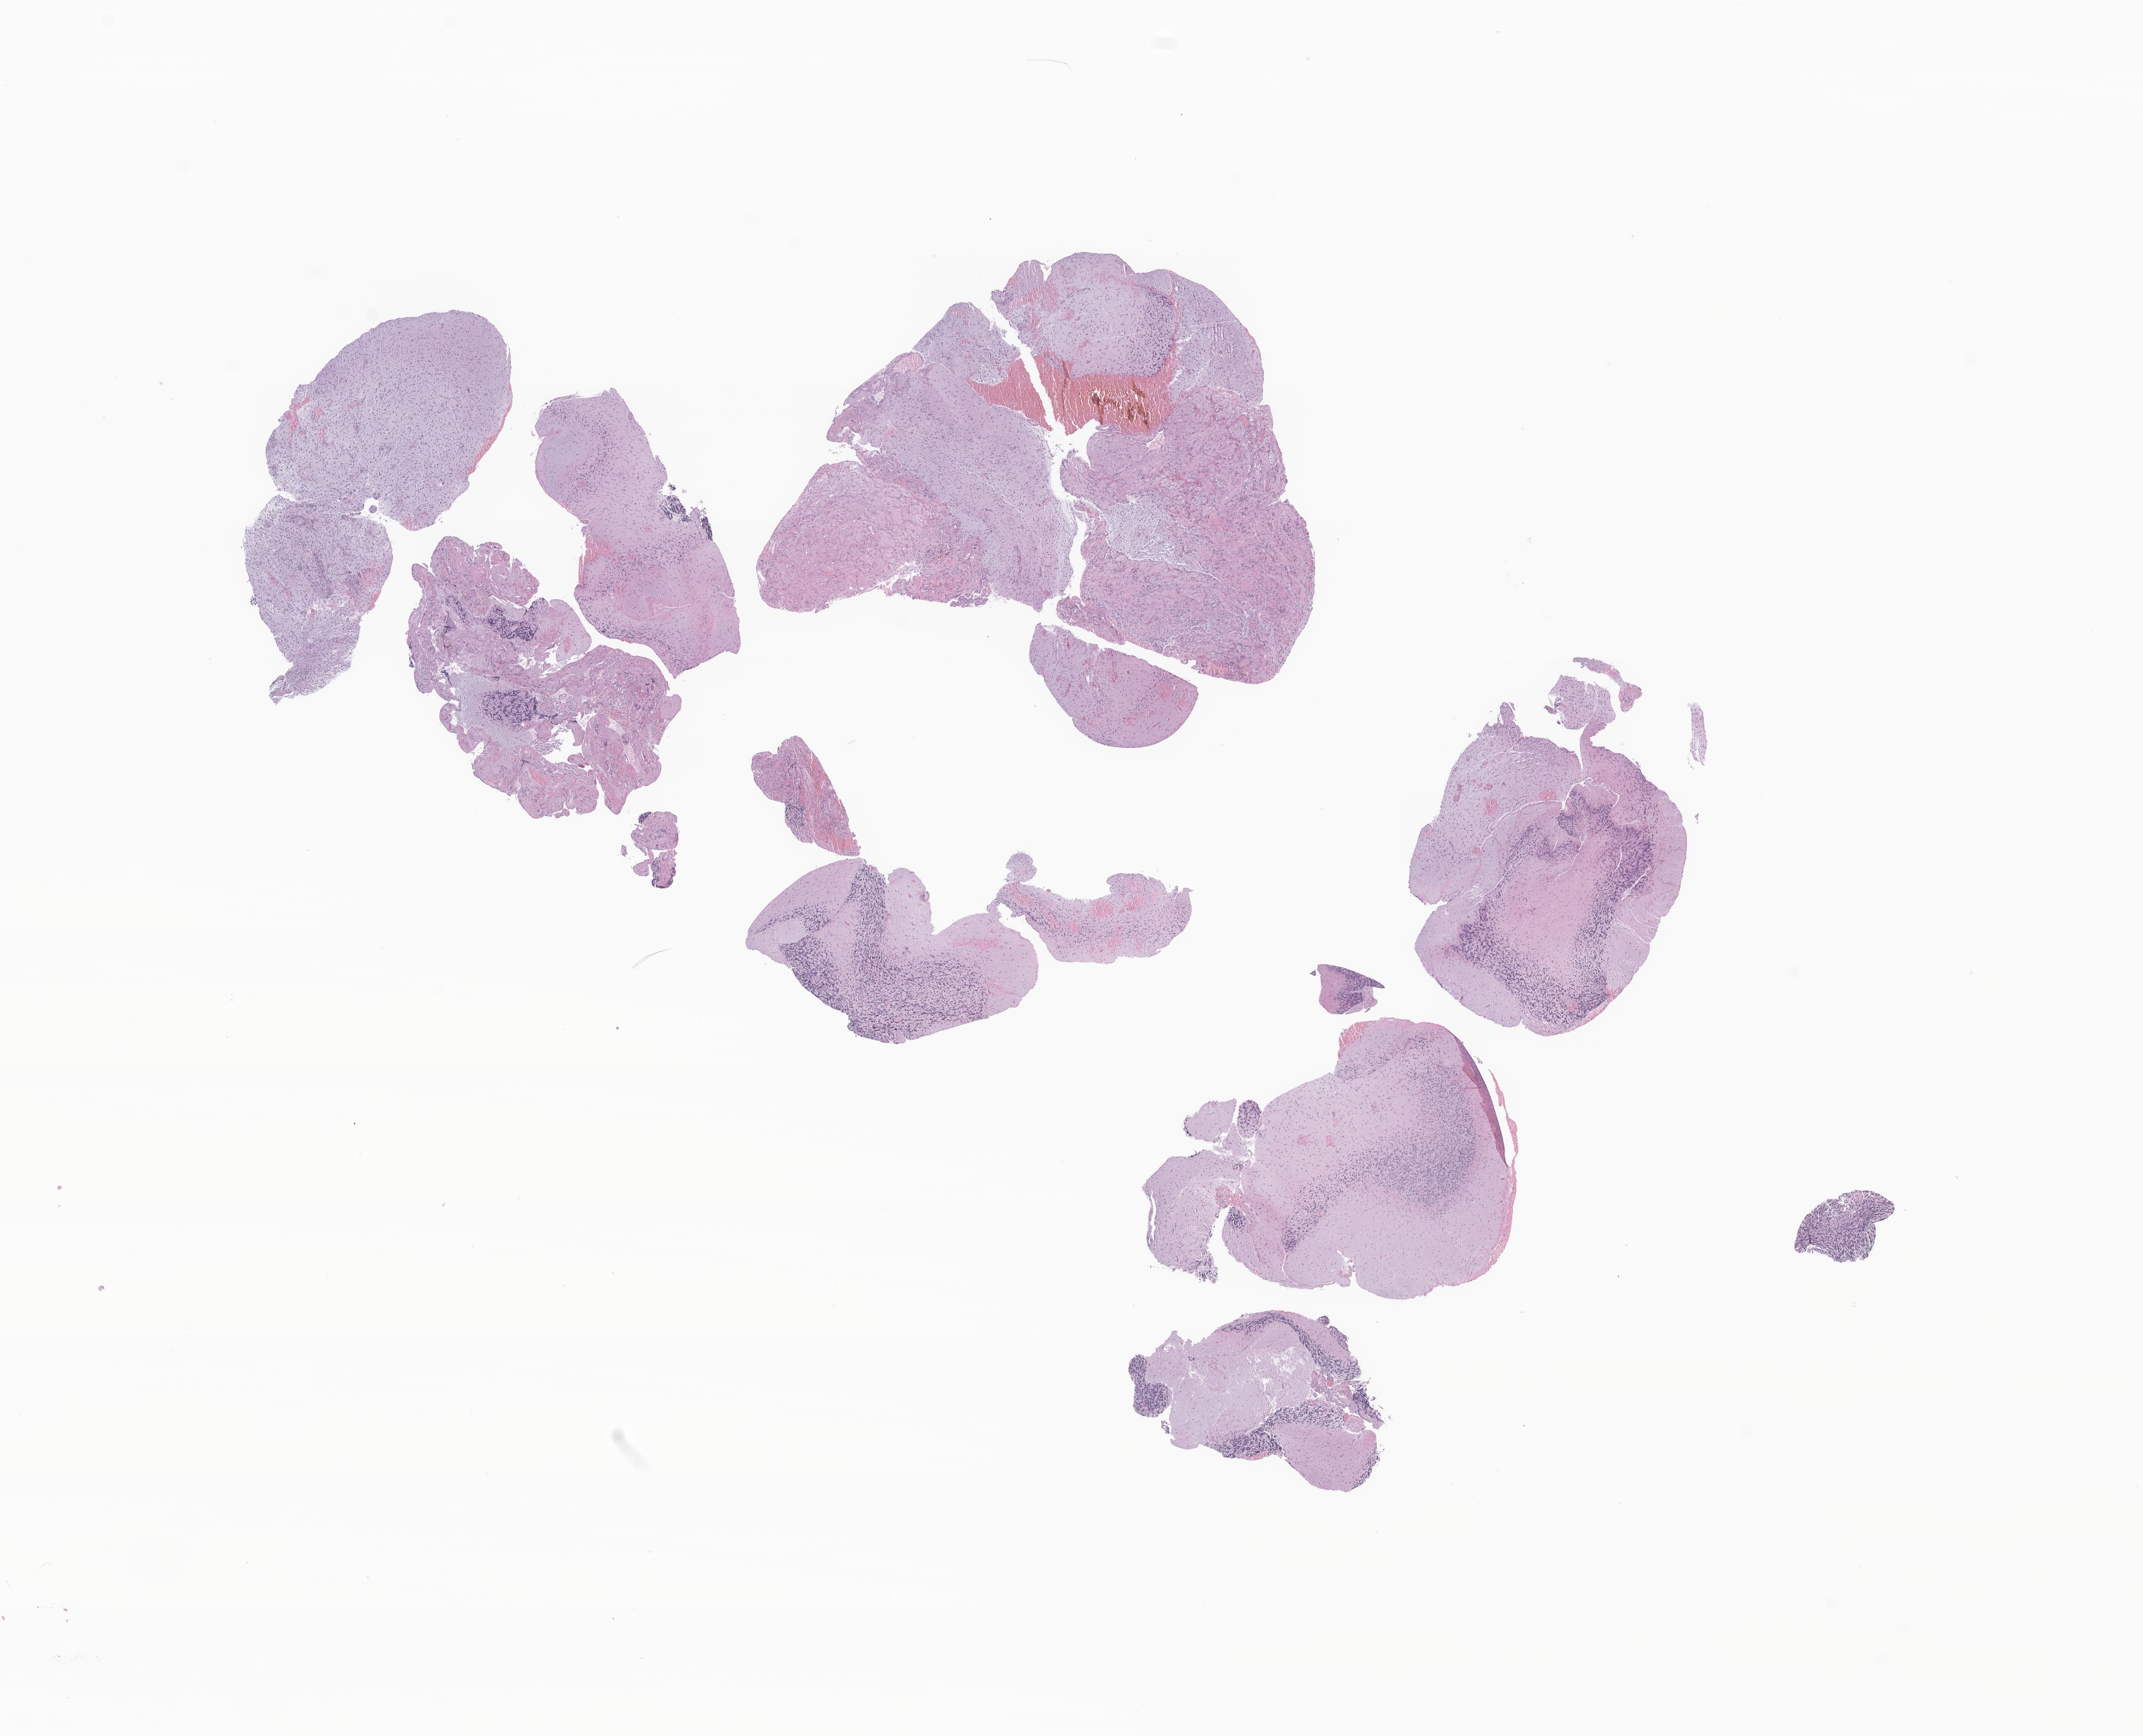
Digitized hematoxylin and eosin (H&E)-stained section of tumor tissue from the brain — low-resolution overview of the scanned area, about 17.0 x 13.7 mm. Formalin-fixed paraffin-embedded section. Male patient, age 60 months (5 years).
Recorded diagnosis: Glioma, malignant.